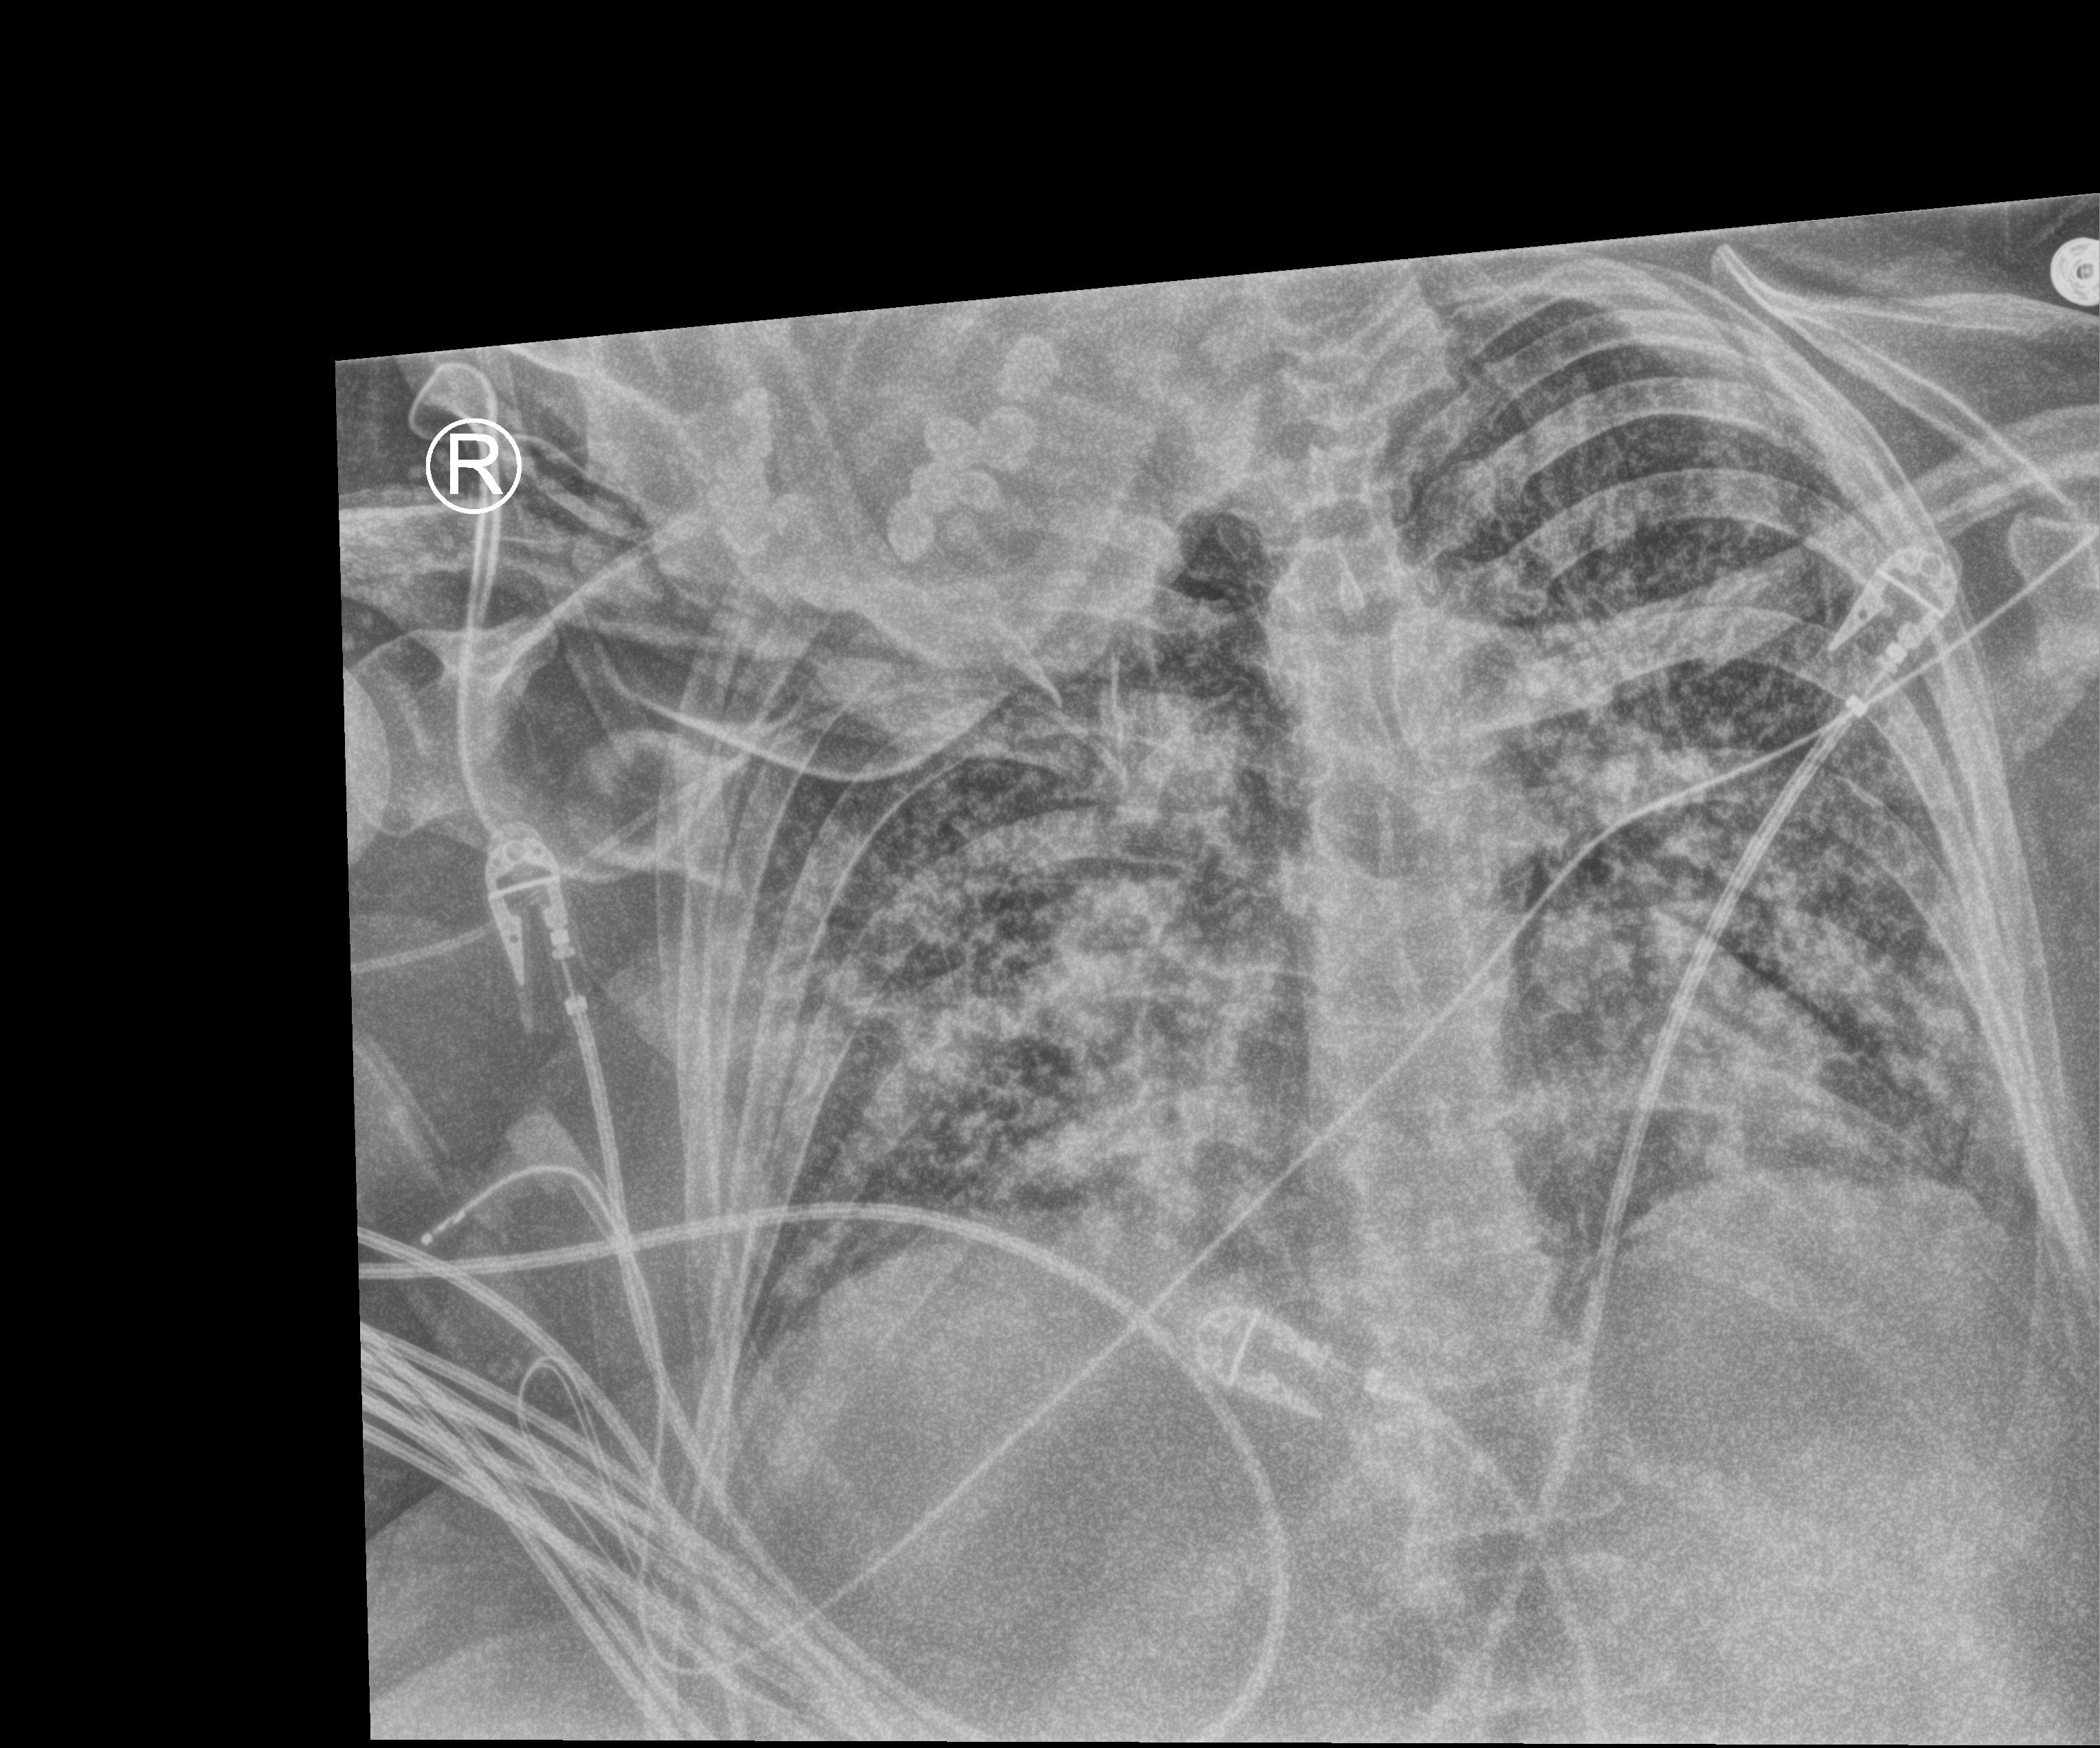
Portable chest radiograph; anteroposterior (AP) projection. Female patient hospitalised with COVID-19, age 60–74 years.
Hospital-stay facts (about this admission, not read from this image; timing relative to this image not recorded): COPD (admission record): no; mechanically ventilated during this hospital stay: yes; smoking status (admission record): never.